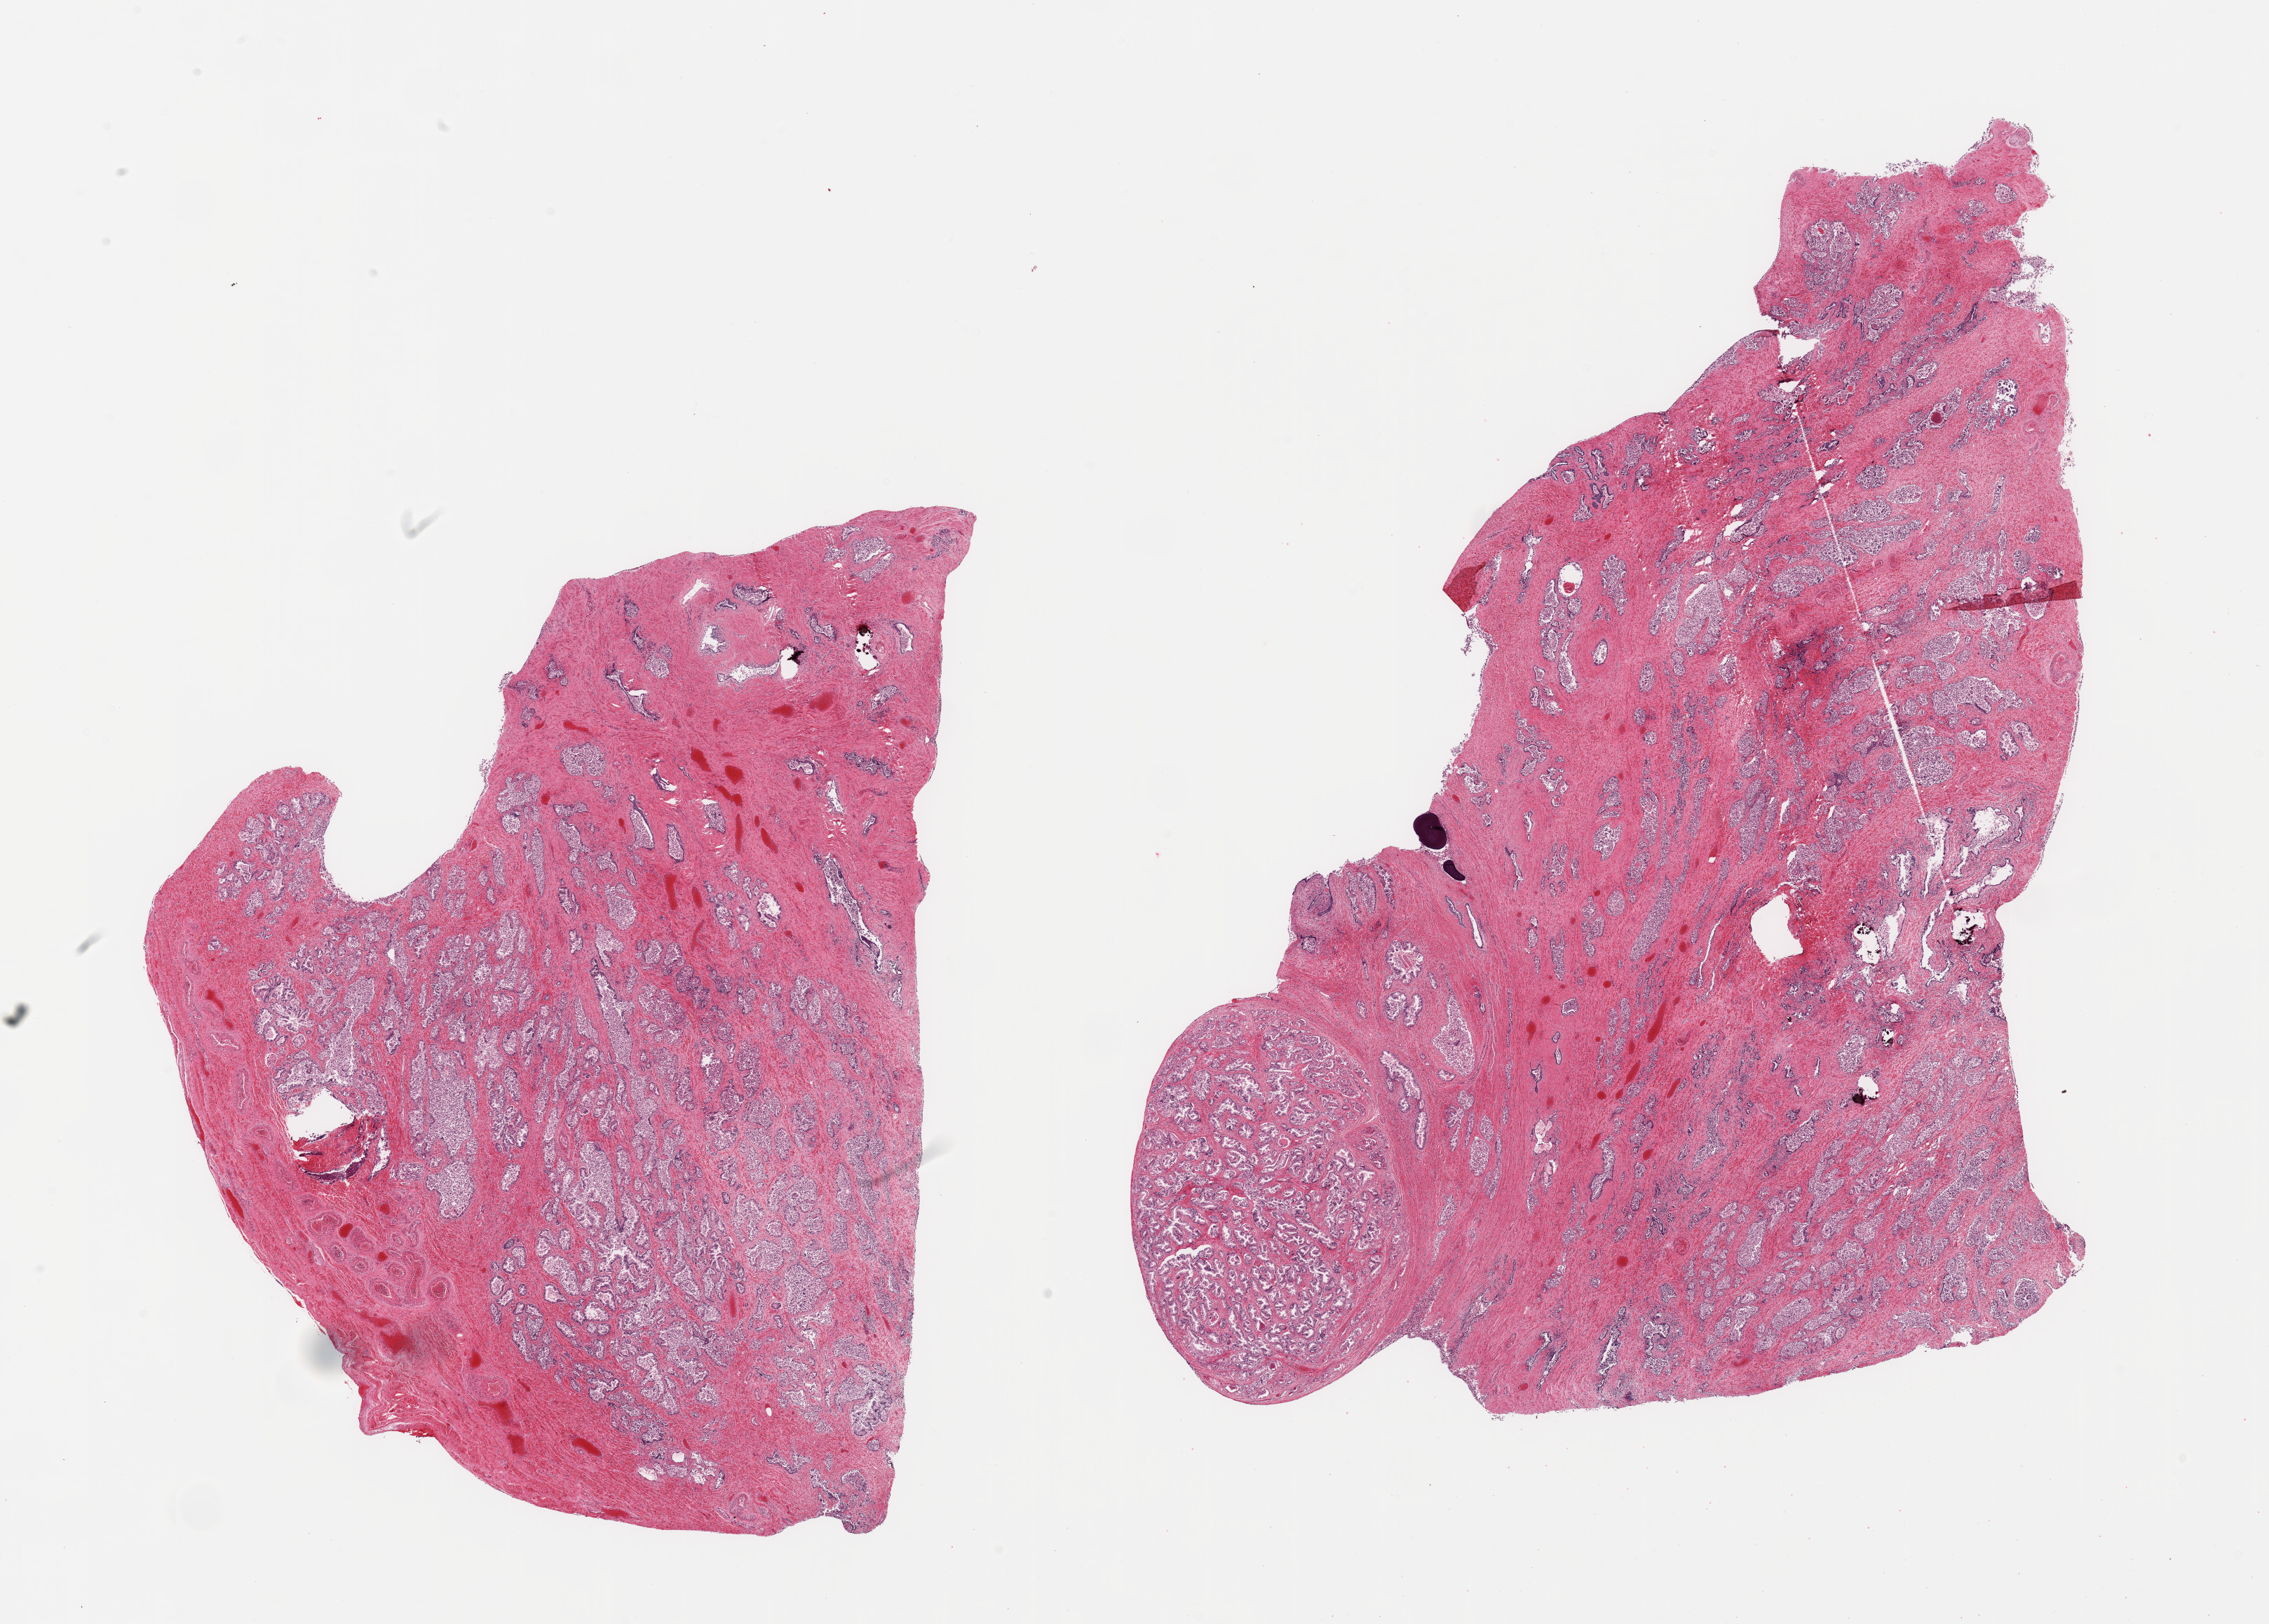
Digitized haematoxylin and eosin-stained section, a low-resolution overview of the entire scanned area, about 25.6 x 18.3 mm, PAXgene-fixed, paraffin-embedded tissue, sampled site (target tissue): prostate, donor tissue sample. Male donor.
- review note (as recorded): 2 pieces, moderately advanced glandular mucosal autolysis, hyperplastic glandular pattern